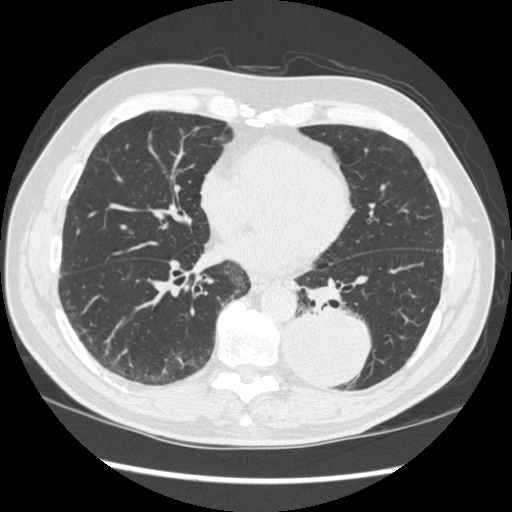
Low-dose screening chest CT, one axial slice; slice 135 of 348 in the series (ordered by position); reconstruction kernel STANDARD; lung window (W 1500 / L -600 HU); 1.25 mm slice thickness; 512 × 512 image matrix.
Structures marked on this image (outlined manually by an expert reader):
- lesion 1 (tumor, lower lobe of left lung): bounding box [x1, y1, x2, y2] px = [283, 309, 371, 387]